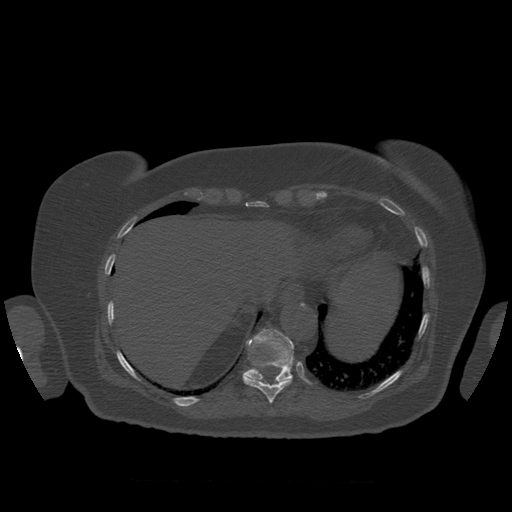
CT including the spine, one axial slice. Position 333 of 399 along the scan axis. 120 kVp. Bone window (W 1800 / L 400 HU). 1.25 mm slice thickness. 512 × 512 image matrix, field of view 404 × 404 mm. Patient age 81 years. From the clinical record (not read from this slice): primary cancer: renal.
Outlined on this slice (semi-automatic segmentation, software-assisted and operator-edited):
- T10 vertebra: bounding box [x1, y1, x2, y2] px = [243, 376, 293, 404]
- T11 vertebra: [243, 328, 295, 382]